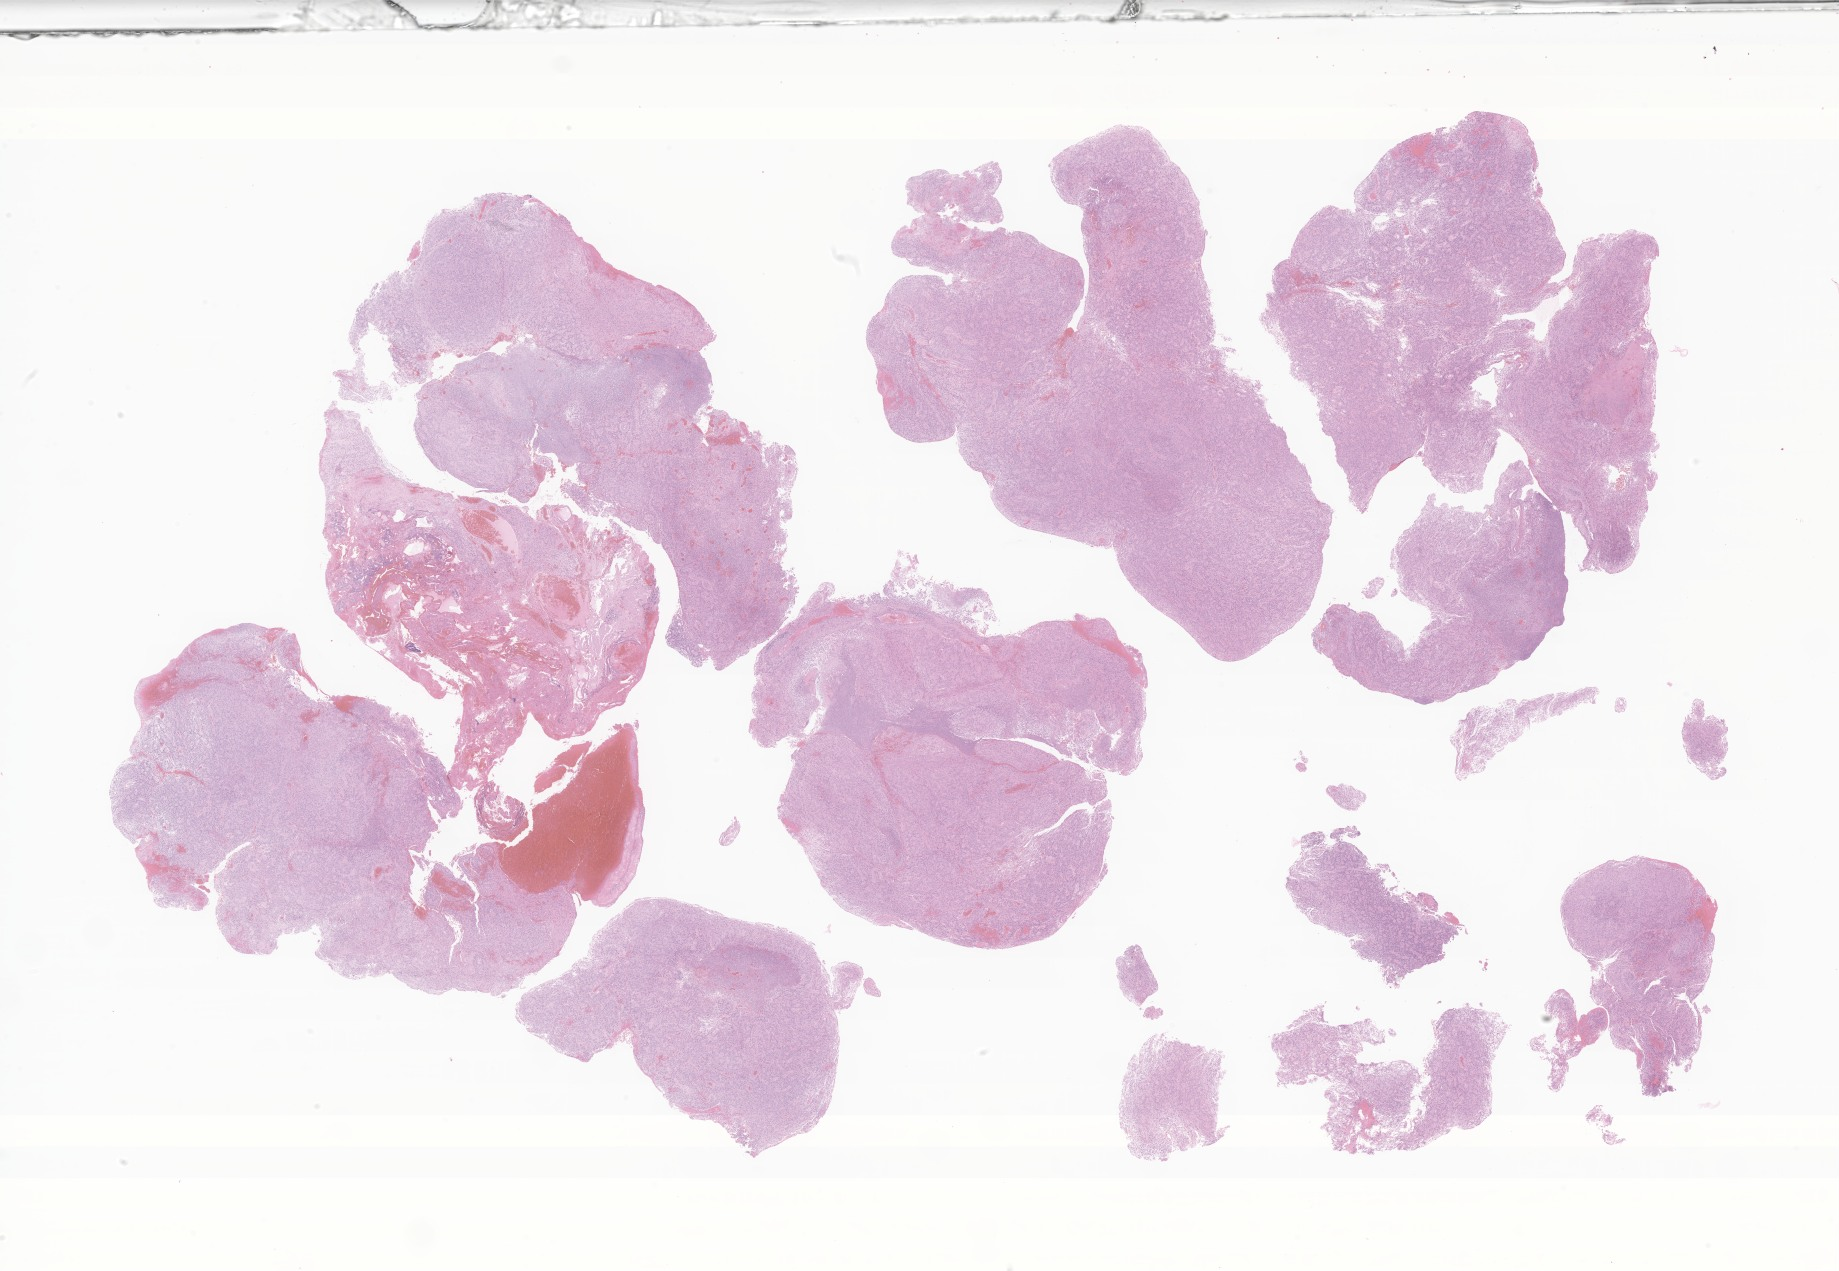
Hematoxylin and eosin (H&E) whole-slide image of tumor tissue from the brain, whole scanned area (about 31.0 x 21.4 mm) shown as a low-resolution overview, formalin-fixed paraffin-embedded section. Patient: female, age 151 months (12 years 7 months).
• diagnosis (ICD-O-3 morphology term): Ependymoma, NOS